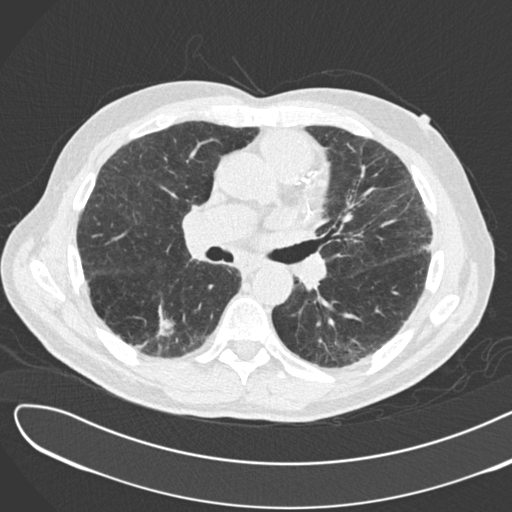
Low-dose screening chest CT, axial slice. Second annual screen. Lung window (W 1500 / L -600 HU). 2 mm slice thickness. 512 × 512 image matrix. Male, age 72 years at enrolment.
Lesion marked by an expert reader, box from (x=137, y=293) to (x=192, y=347) px. The screening reader recorded 2 non-calcified nodules or masses ≥4 mm on this exam (right lower lobe, right lower lobe); which of them this box marks is not recorded. Participant outcome: lung cancer diagnosed 46 days after this screen — squamous cell carcinoma, NOS, right lower lobe, poorly differentiated (G3), stage IB (AJCC 6th edition), 42 mm at pathology.